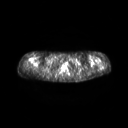
FDG PET of an extremity soft-tissue mass (from a PET/CT study), one axial slice. Slice 214 of 267 in the series (ordered by position). 3.27 mm slice thickness. 128 × 128 image matrix, field of view 600 × 600 mm. Patient: female, 28 years. From the clinical record (not read from this slice): histological type: malignant fibrous histiocytoma; grade: low; site of the primary tumour: left arm.
Annotated regions visible in this slice (expert contour drawn on MRI and transferred to this co-registered scan by the dataset authors):
- gross tumour volume (mass): bounding box <99,66,103,69> (left, top, right, bottom; pixels)